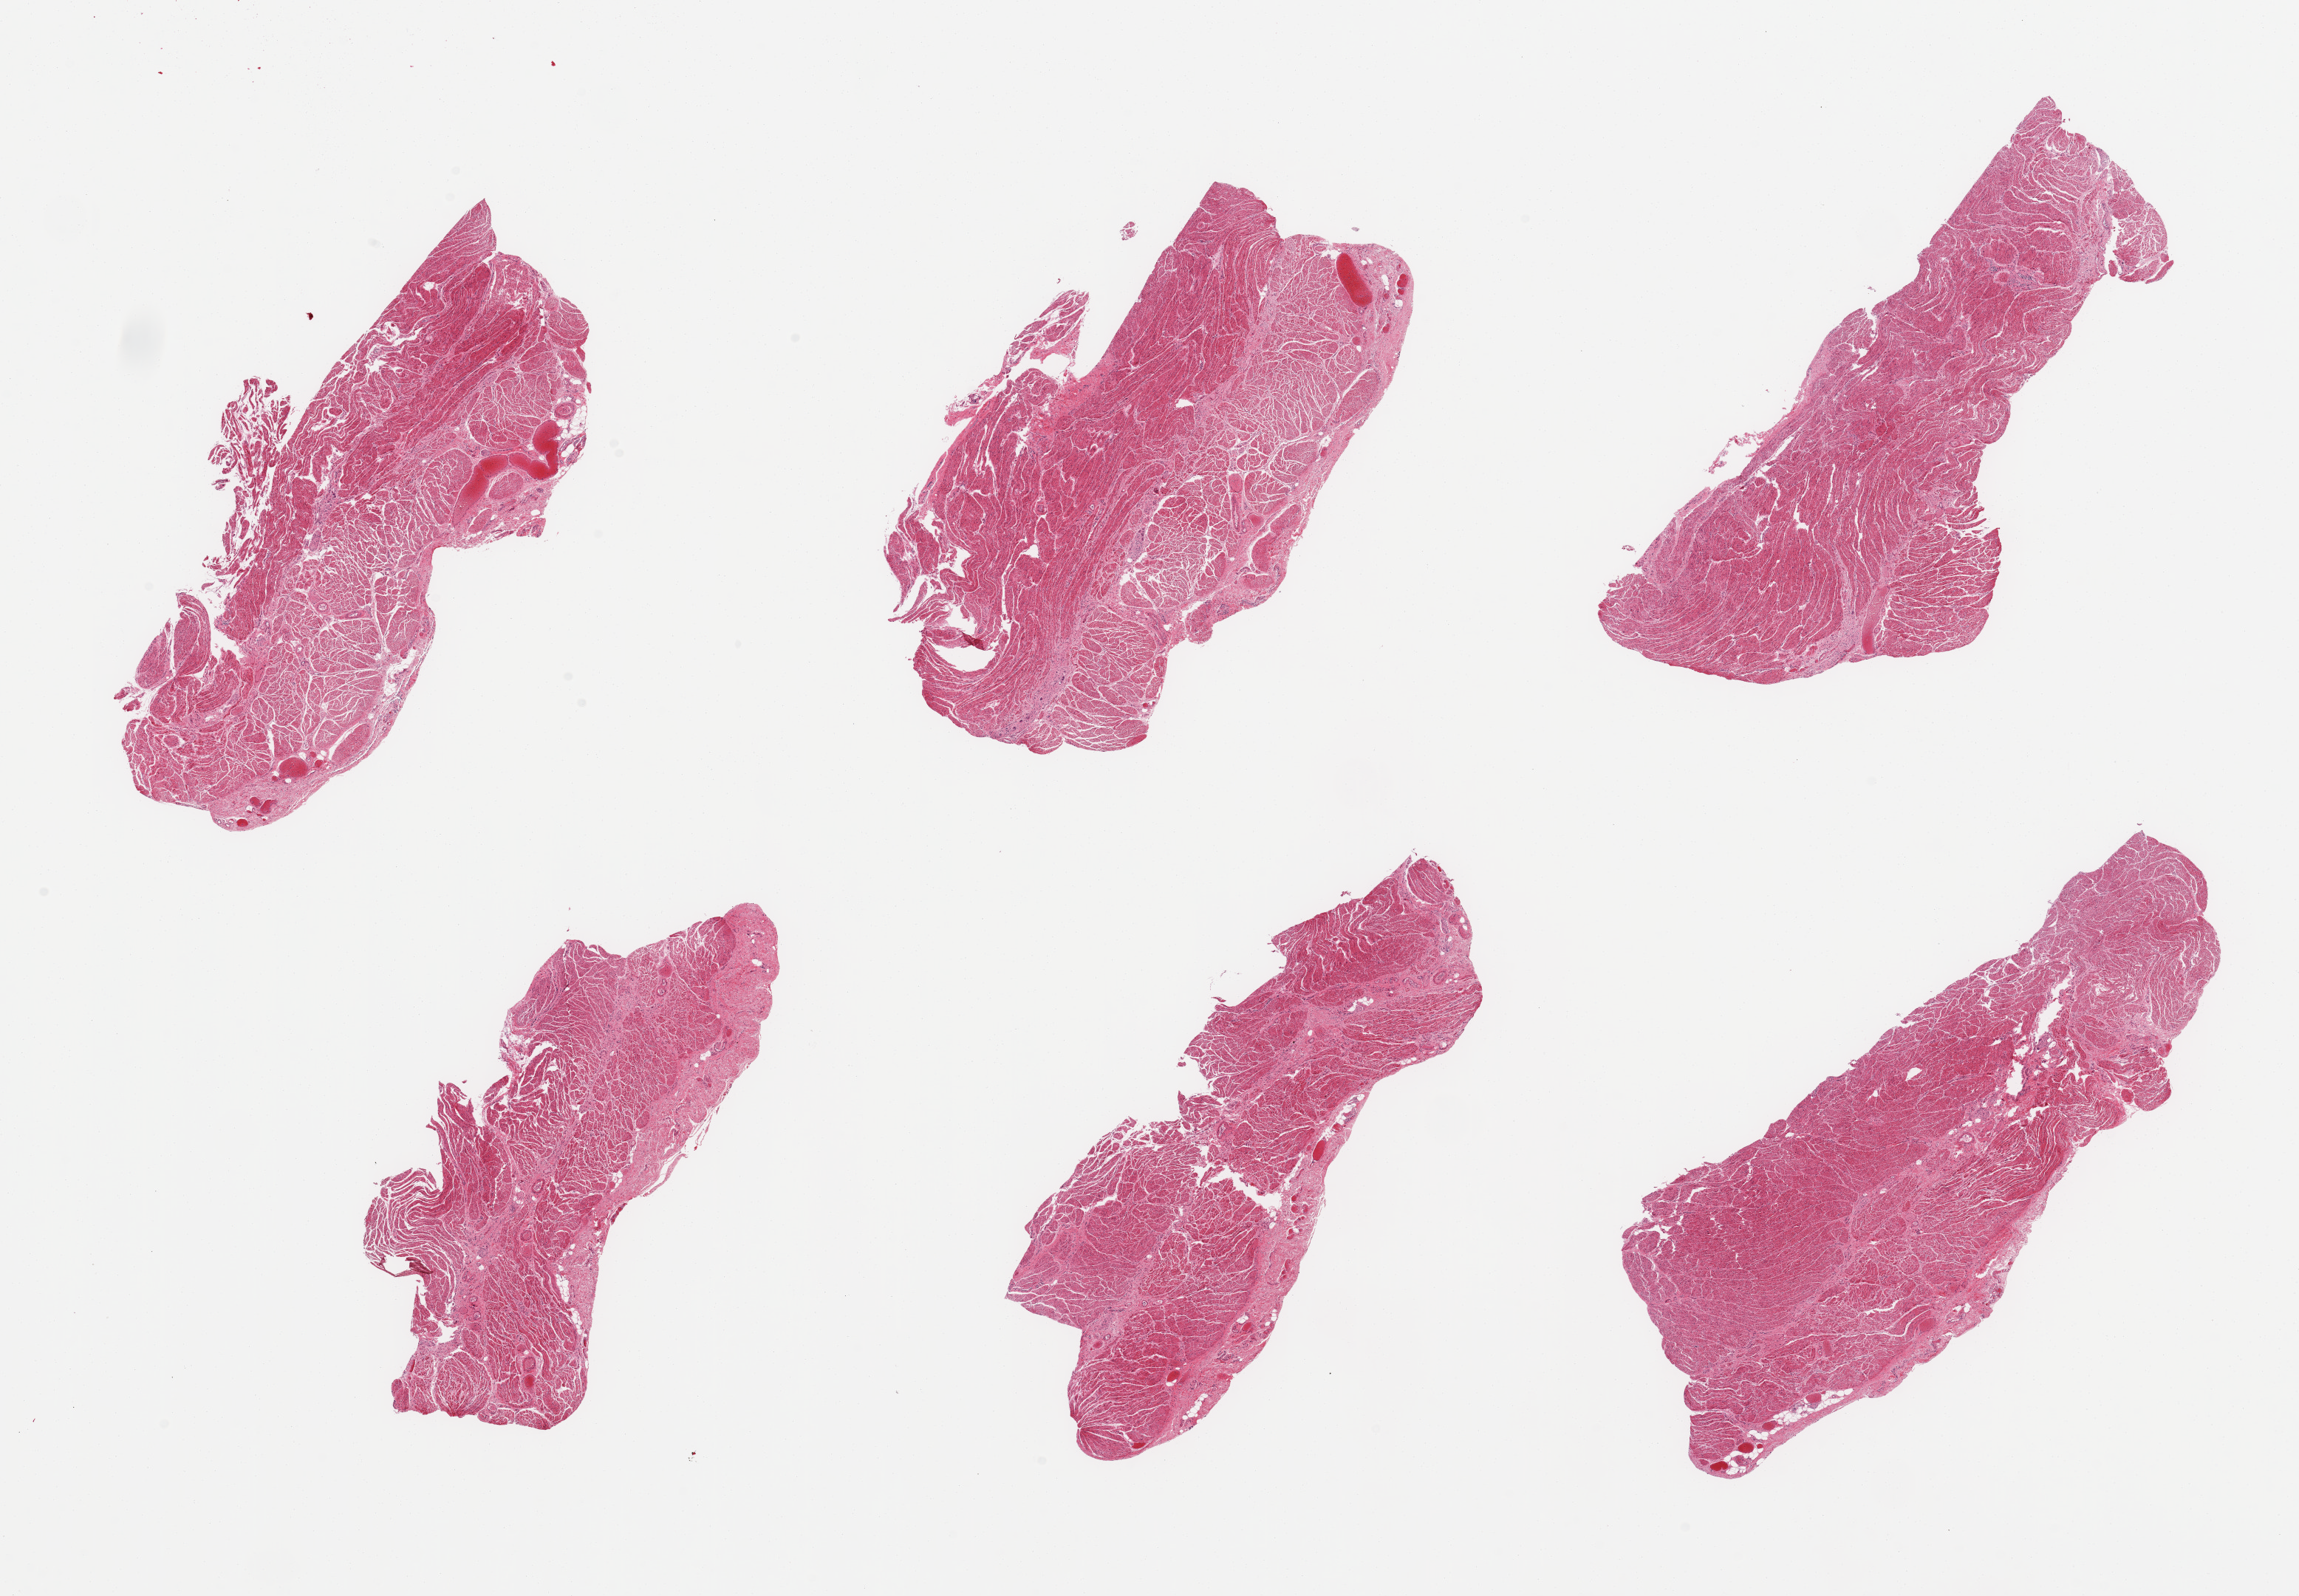
Digitized H&E-stained section, a low-resolution overview of the entire scanned area, about 24.6 x 17.1 mm; PAXgene-fixed, paraffin-embedded tissue; sampled site (target tissue): gastroesophageal junction; donor tissue sample. Donor: male.
• reviewer comment on this tissue sample: 6 pieces, confirmed target muscularis